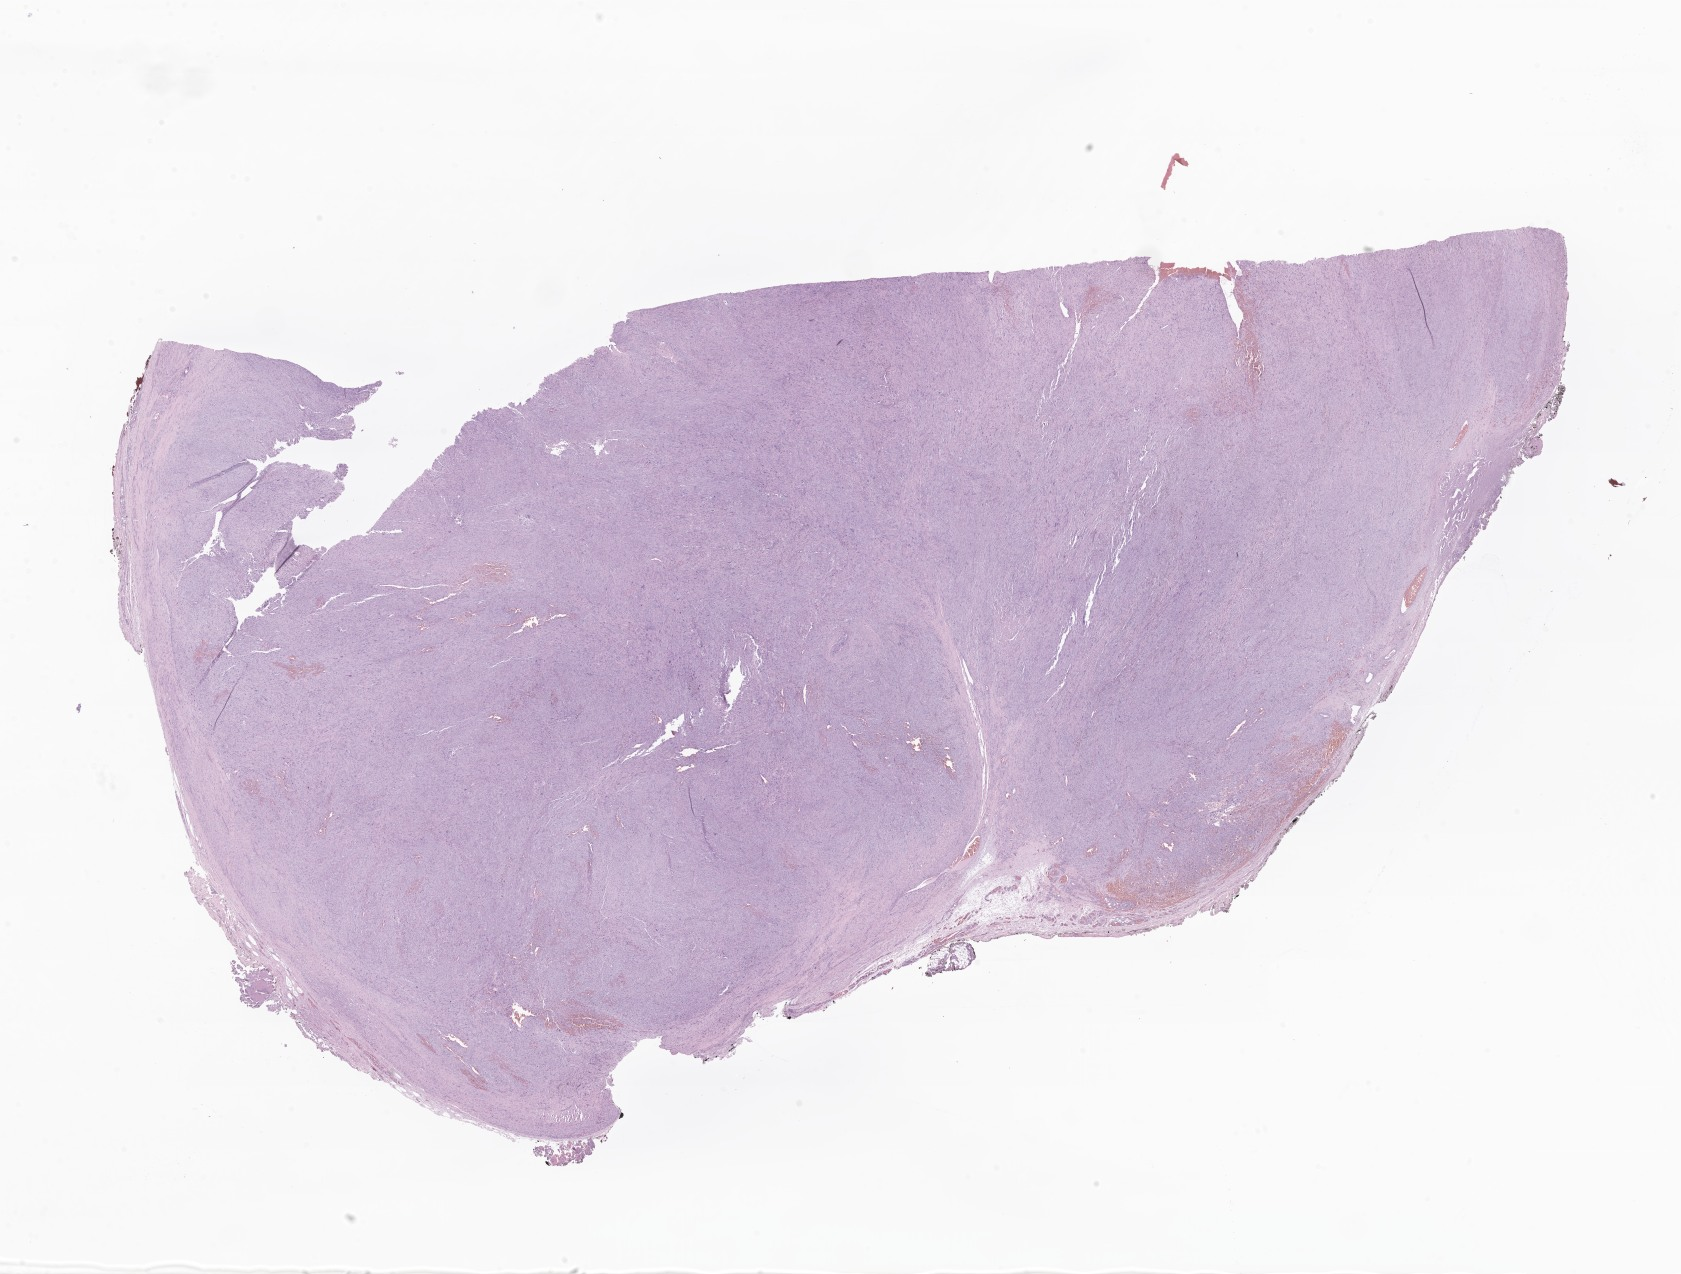
Digitized haematoxylin and eosin-stained section of tumor tissue from the soft tissue of upper extremity, shown as a low-resolution overview of the whole scanned area (about 28.4 x 21.5 mm), formalin-fixed paraffin-embedded section. Patient: female, age 84 months (7 years).
Diagnosis (ICD-O-3 morphology term): Sarcoma, NOS. Tissue or organ of origin (case record): connective, subcutaneous and other soft tissues of upper limb and shoulder.